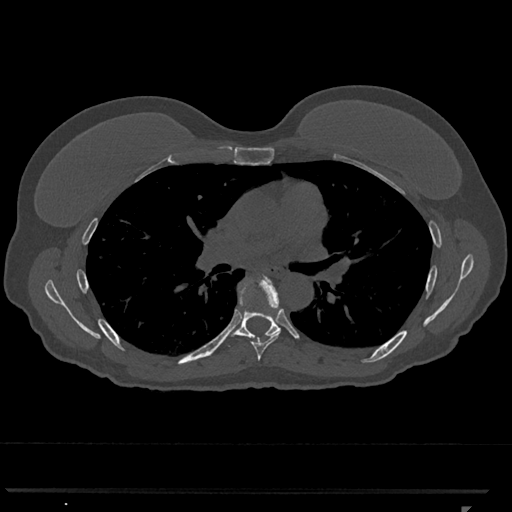
CT including the spine, one axial slice. Position 739 of 793 along the scan axis. Reconstruction kernel Br40s/3. Bone window (W 1800 / L 400 HU). 0.5 mm slice thickness. 512 × 512 image matrix. Female patient, age 62 years. Case-level facts recorded for this patient, not image findings: primary cancer: renal.
Outlined on this slice (semi-automatically segmented with operator editing):
- T6 vertebra: bounding box [x1, y1, x2, y2] px = [238, 277, 281, 361]
- T7 vertebra: [226, 280, 280, 347]